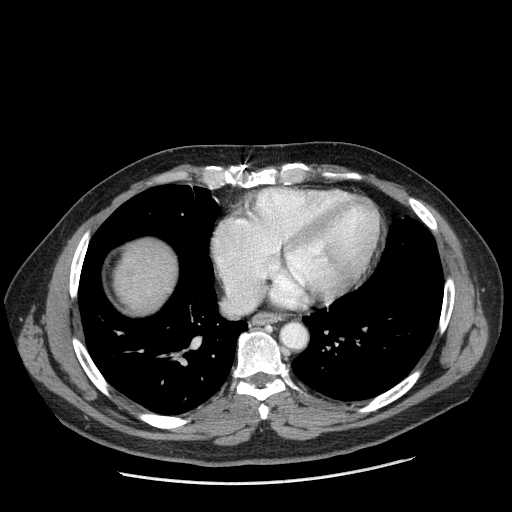
Contrast-enhanced abdominal CT (liver protocol), one axial slice; 120 kVp; one of 2 acquisitions stored at this slice position; soft-tissue window (W 400 / L 40 HU); 512 × 512 image matrix, field of view 400 × 400 mm. From the clinical record (not read from this slice): diagnosis: hepatocellular carcinoma (patient treated with transarterial chemoembolisation; whether this scan precedes or follows treatment is not stated here); TNM stage (as recorded): Stage-II; Child-Pugh class: A; tumour differentiation: moderately differentiated; tumour nodularity: multinodular.
Structures marked on this image (semi-automatically segmented with operator editing):
- liver parenchyma outside the tumour (the mass and vessels are separate outlines, so this box may not span the whole liver): bounding box (x1, y1, x2, y2) in pixels: (114, 238, 176, 312)